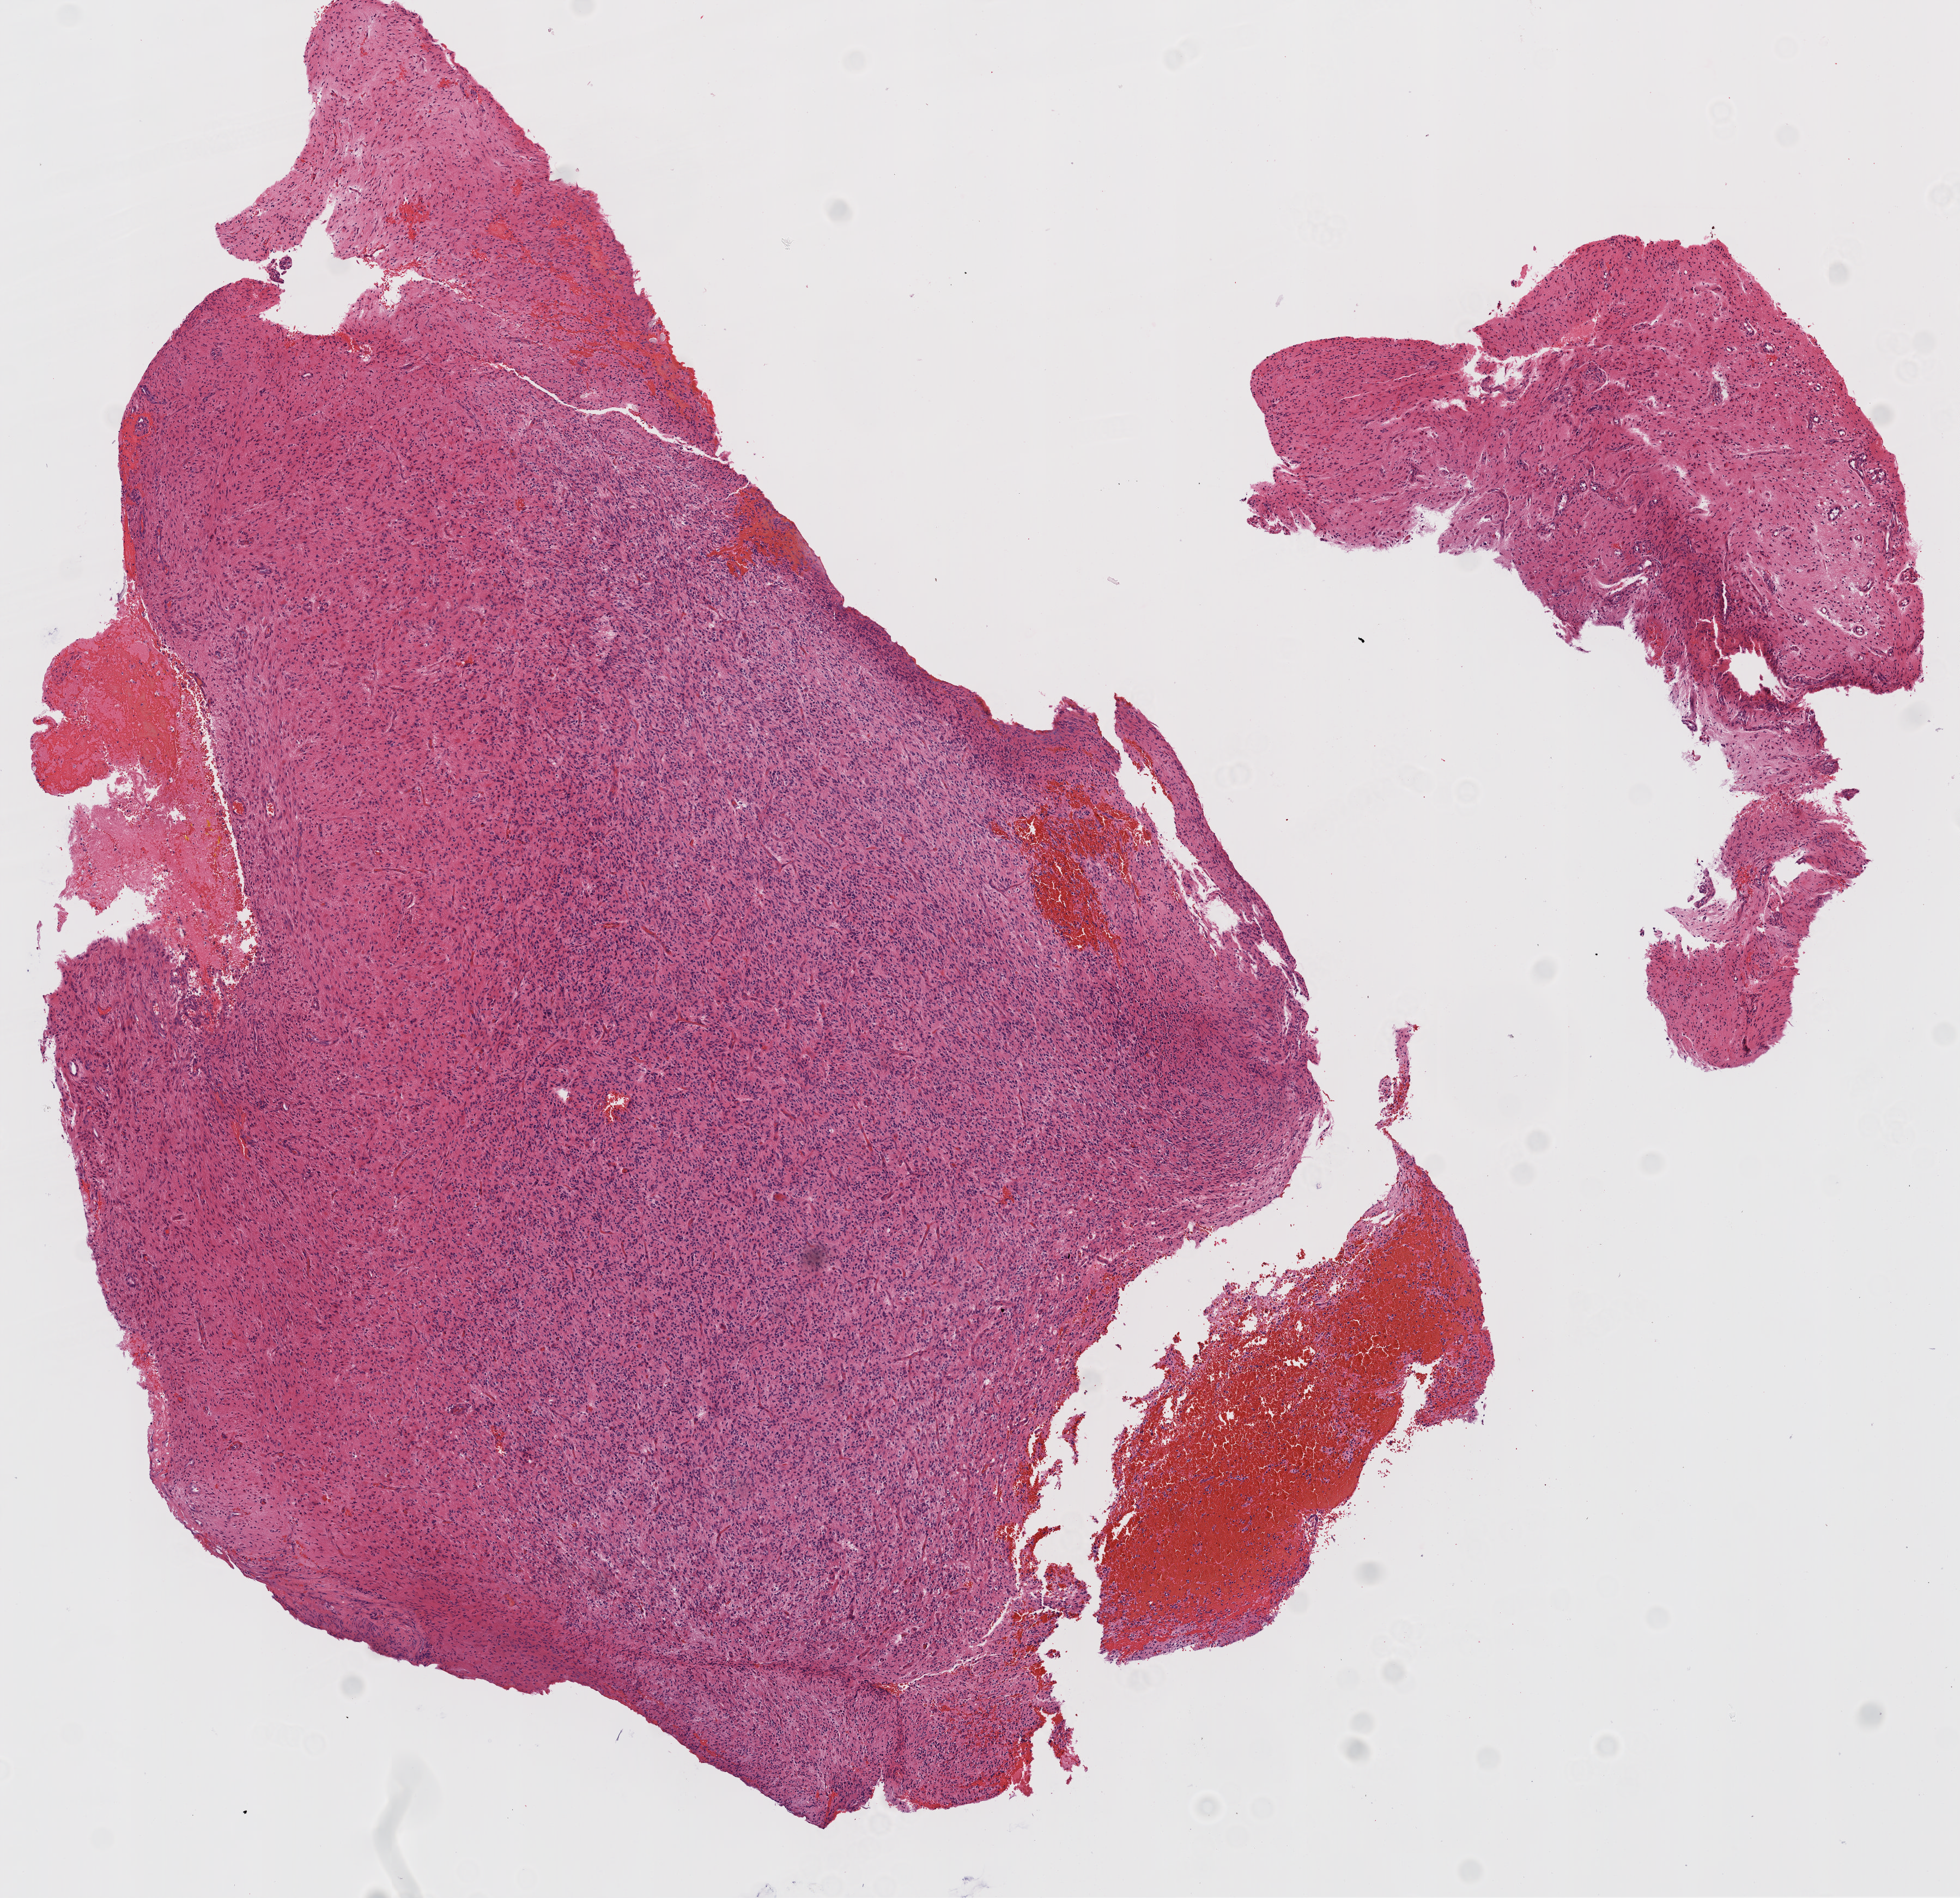
H&E whole-slide image, shown as a low-resolution overview of the whole scanned area (about 7.3 x 7.0 mm, from a 20x scan); FFPE section; brain, primary tumour sample. Female patient; age at initial diagnosis 63 years.
- pathologic diagnosis: Glioblastoma